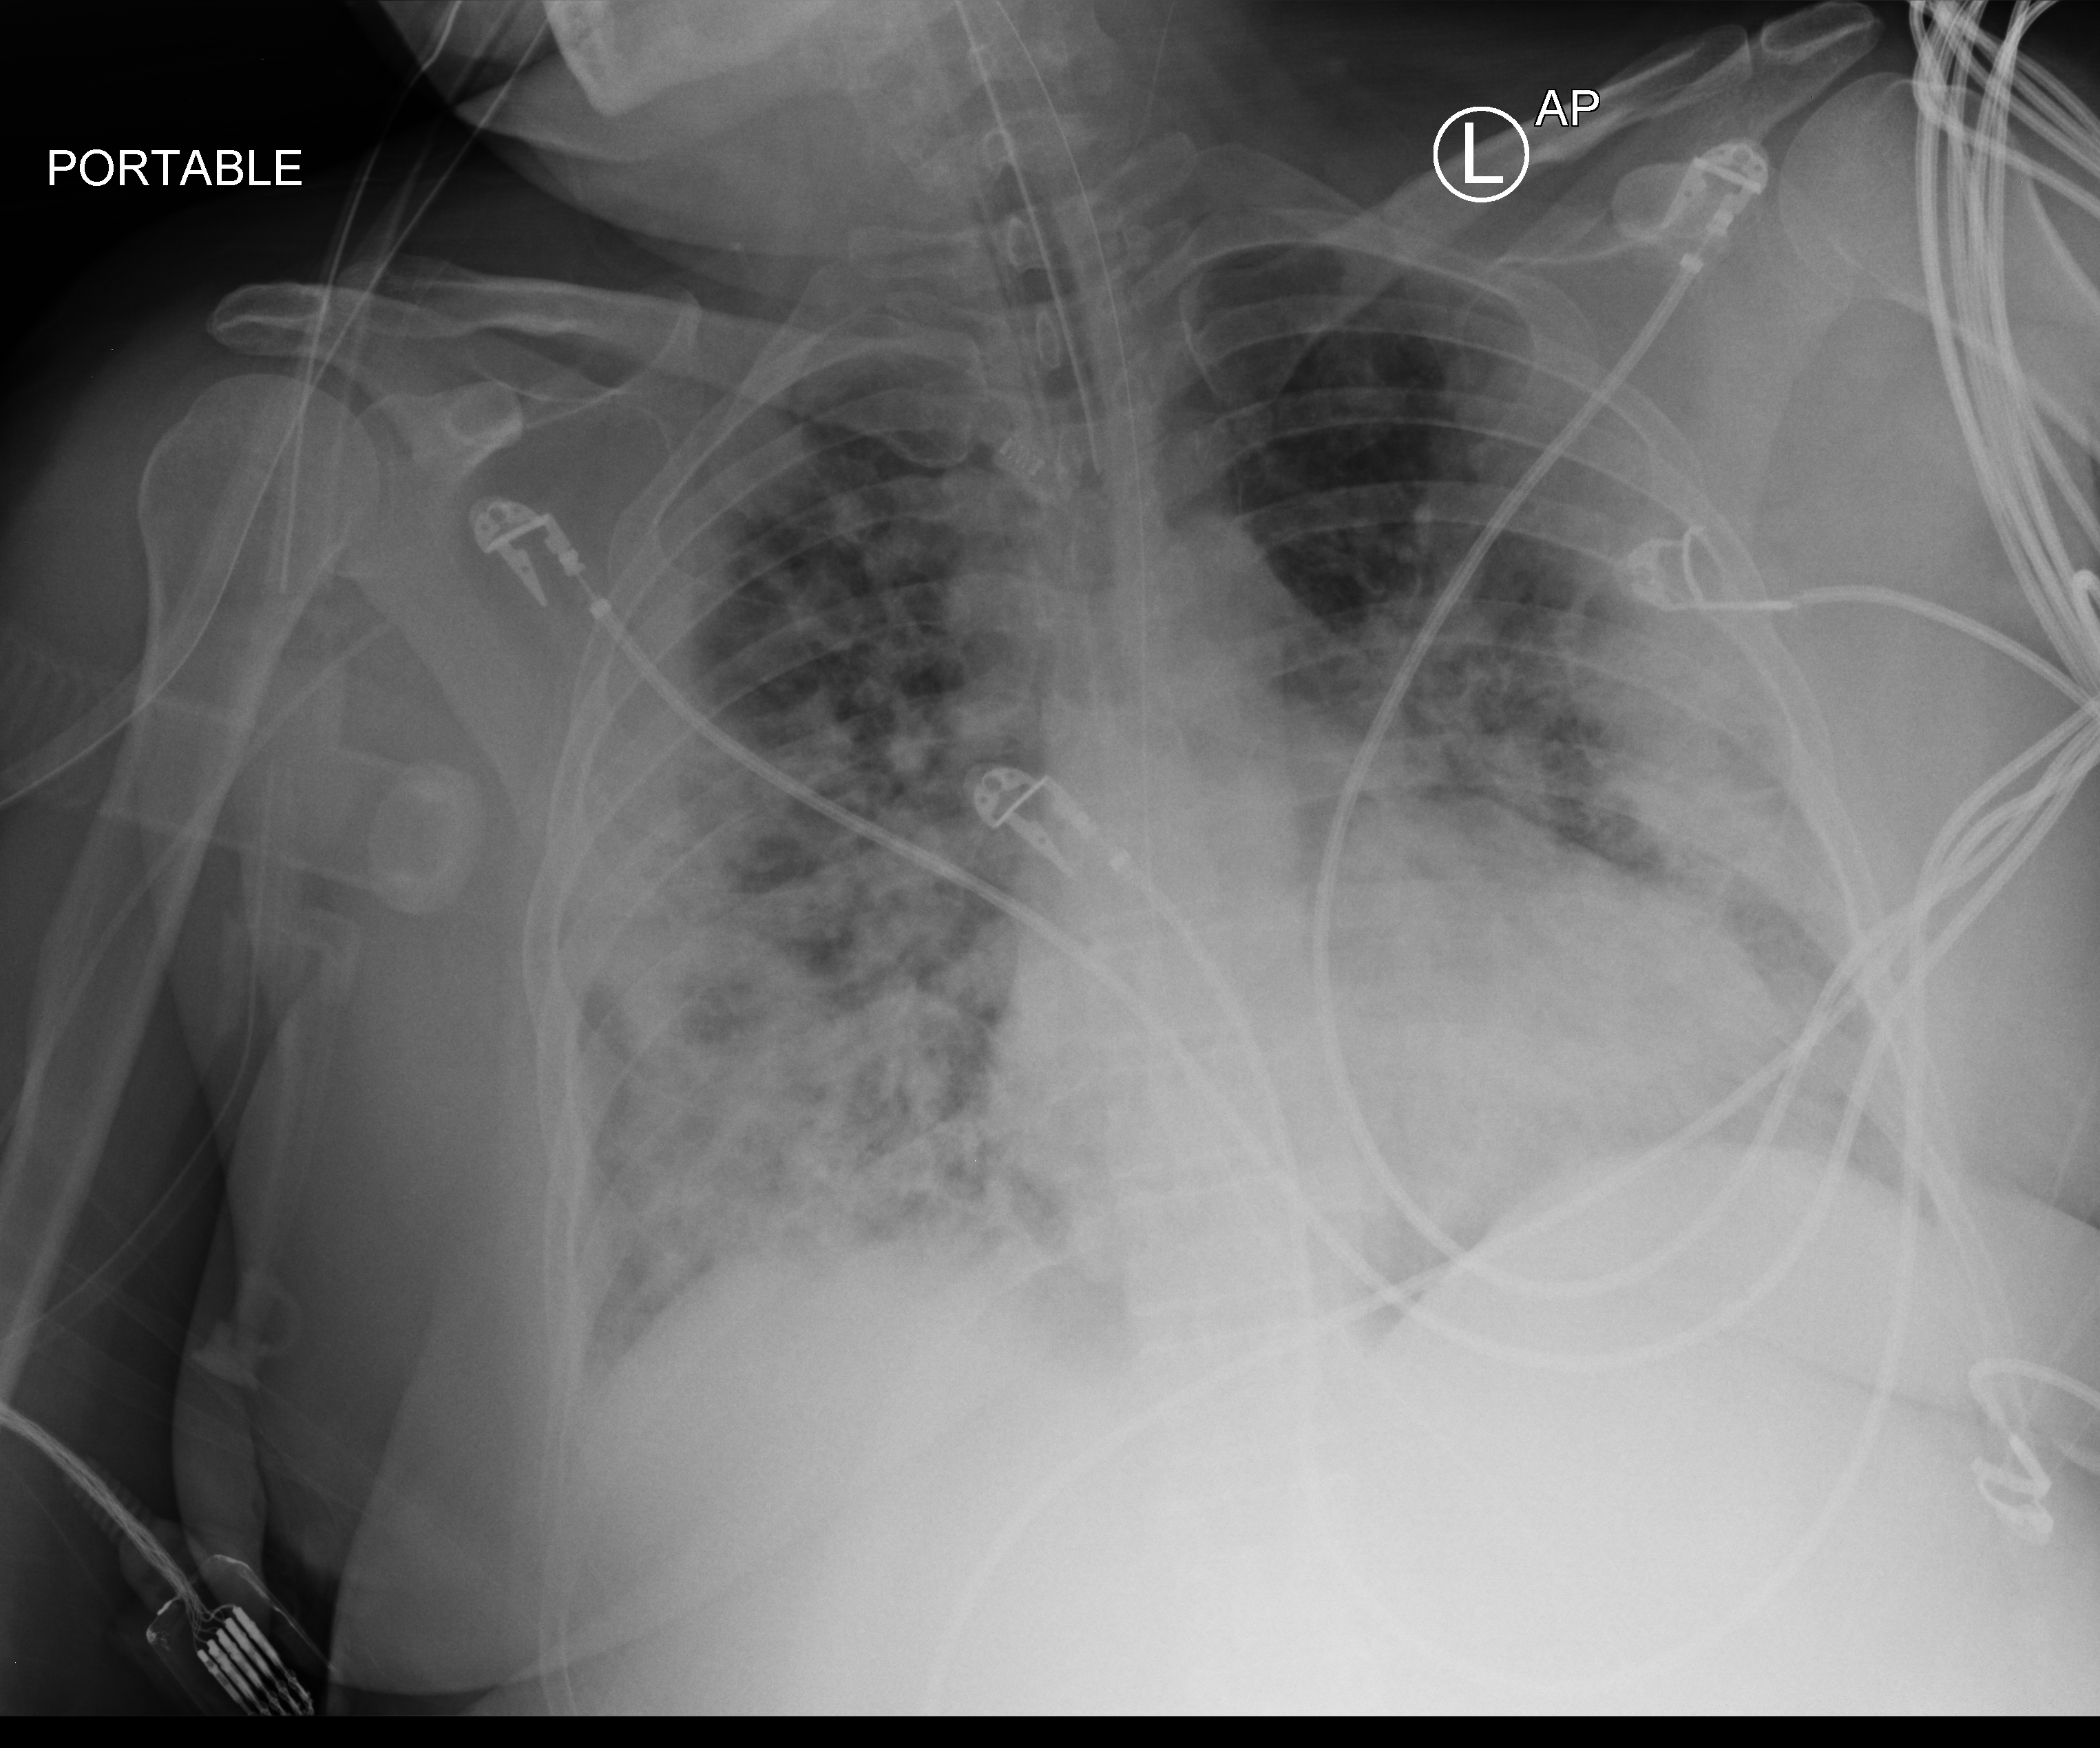
Chest X-ray (portable); anteroposterior (AP) projection. Female patient hospitalised with COVID-19, age 18–59 years.
Hospital-stay facts (about this admission, not read from this image; timing relative to this image not recorded):
- mechanically ventilated during this hospital stay: yes
- admitted to intensive care during this hospital stay: yes
- chronic kidney disease (admission record): no